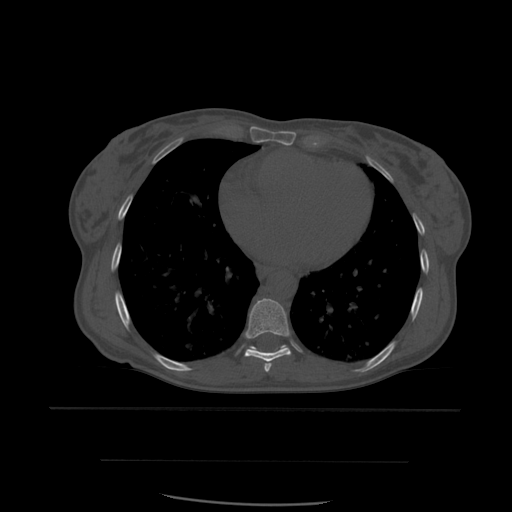
CT including the spine, one axial slice; position 353 of 574 along the scan axis; bone window (W 1800 / L 400 HU); 1.25 mm slice thickness; 512 × 512 image matrix, field of view 392 × 392 mm. Patient age 48 years. Case-level facts recorded for this patient, not image findings: primary cancer: lung.
Annotated regions visible in this slice (semi-automatically segmented with operator editing):
- T7 vertebra: box from (x=265, y=363) to (x=271, y=372) px
- T8 vertebra: (x=244, y=298)–(x=292, y=371)
- T9 vertebra: (x=248, y=346)–(x=288, y=352)